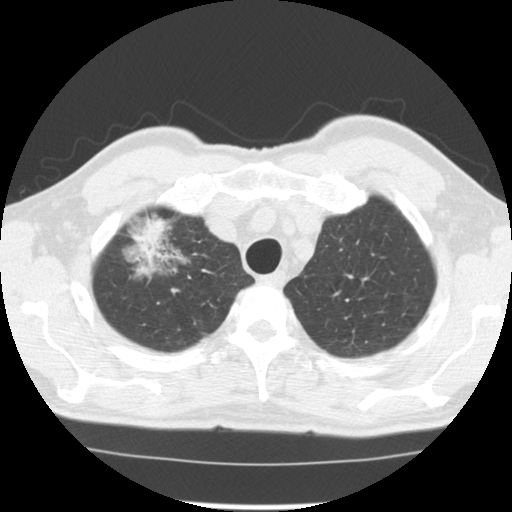
Low-dose screening chest CT, one axial slice; position 106 of 128 along the scan axis; lung window (W 1500 / L -600 HU); 512 × 512 image matrix.
Annotated regions visible in this slice (outlined manually by an expert reader):
- lesion 1 (tumor, upper lobe of right lung): bounding box (x1, y1, x2, y2) in pixels: (136, 219, 169, 257)